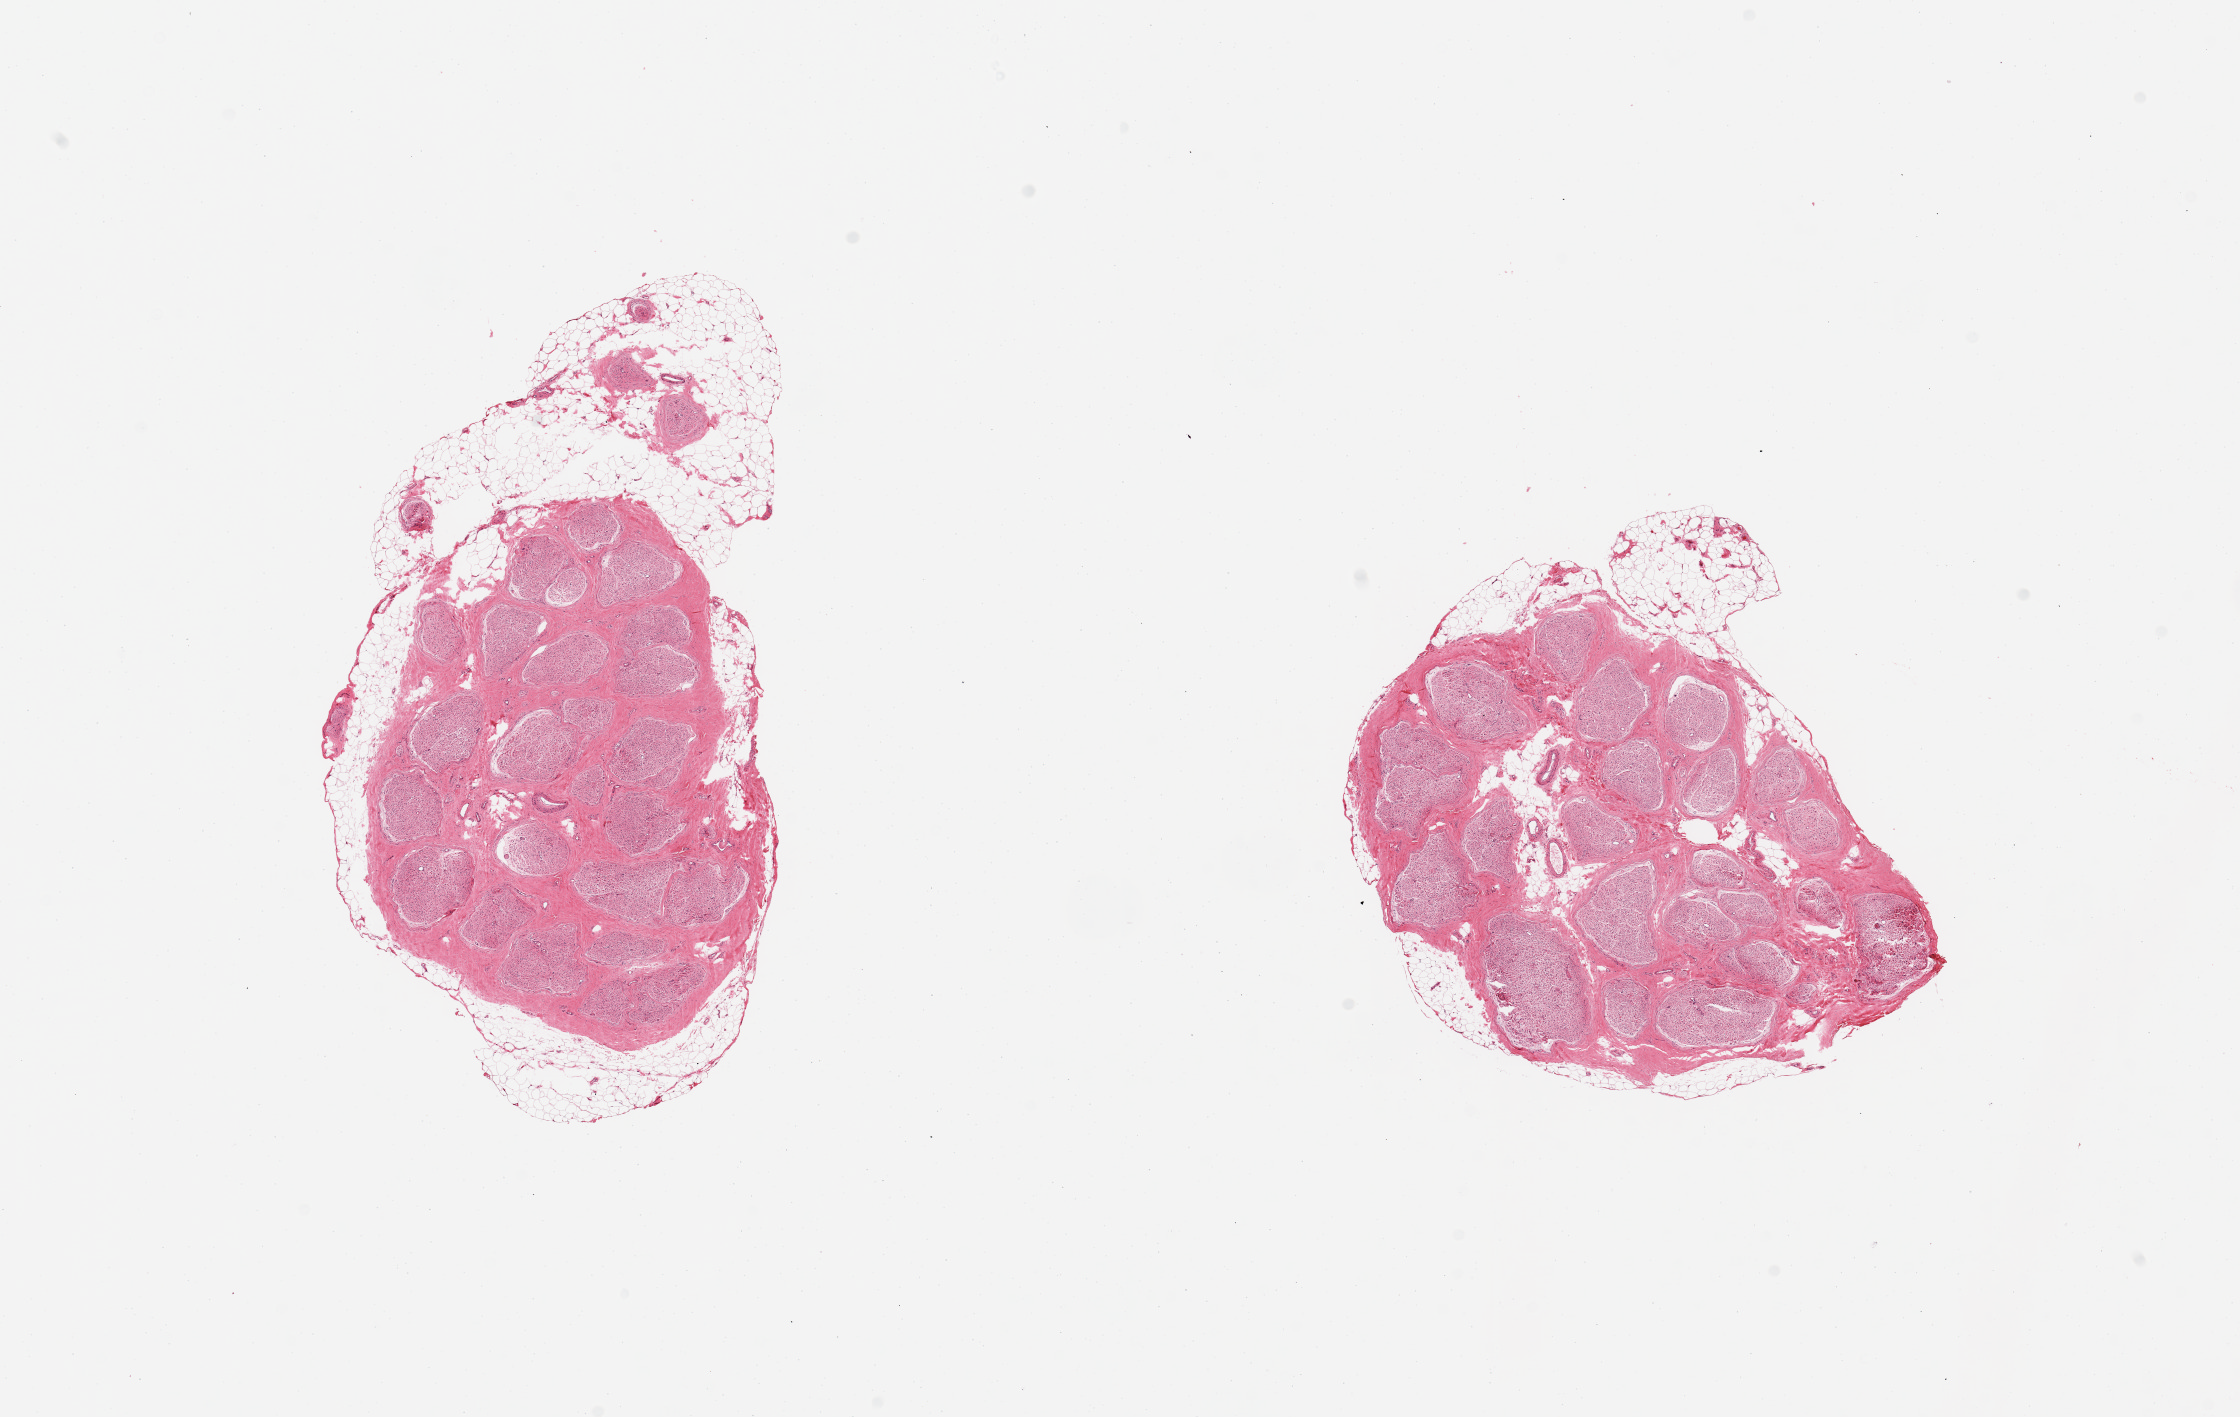
Whole-slide image, H&E stain — shown as a low-resolution overview of the whole scanned area (about 17.7 x 11.2 mm, from a 20x scan); PAXgene-fixed paraffin-embedded (PFPE) section; sampled site (target tissue): tibial nerve; donor tissue sample. Donor sex: male.
* pathologist's review note for this sample: 2 pieces; 20% and 10% external fat